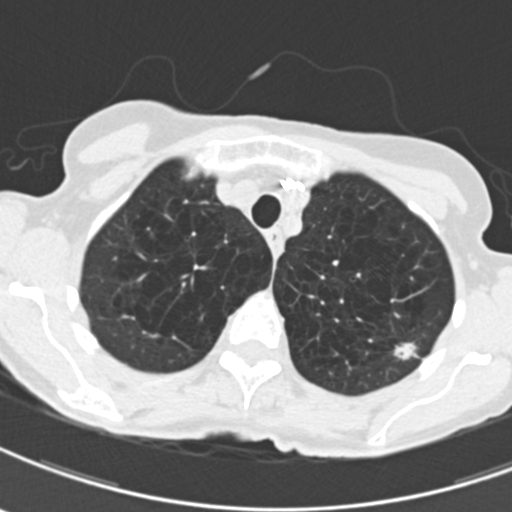
Low-dose screening chest CT, one axial slice; position 164 of 203 along the scan axis; reconstruction kernel B30f; lung window (W 1500 / L -600 HU); 2 mm slice thickness; 512 × 512 image matrix, field of view 279 × 279 mm.
Outlined on this slice (expert manual segmentation):
- lesion 1 (tumor, upper lobe of left lung): bounding box (x1, y1, x2, y2) in pixels: (394, 343, 418, 360)